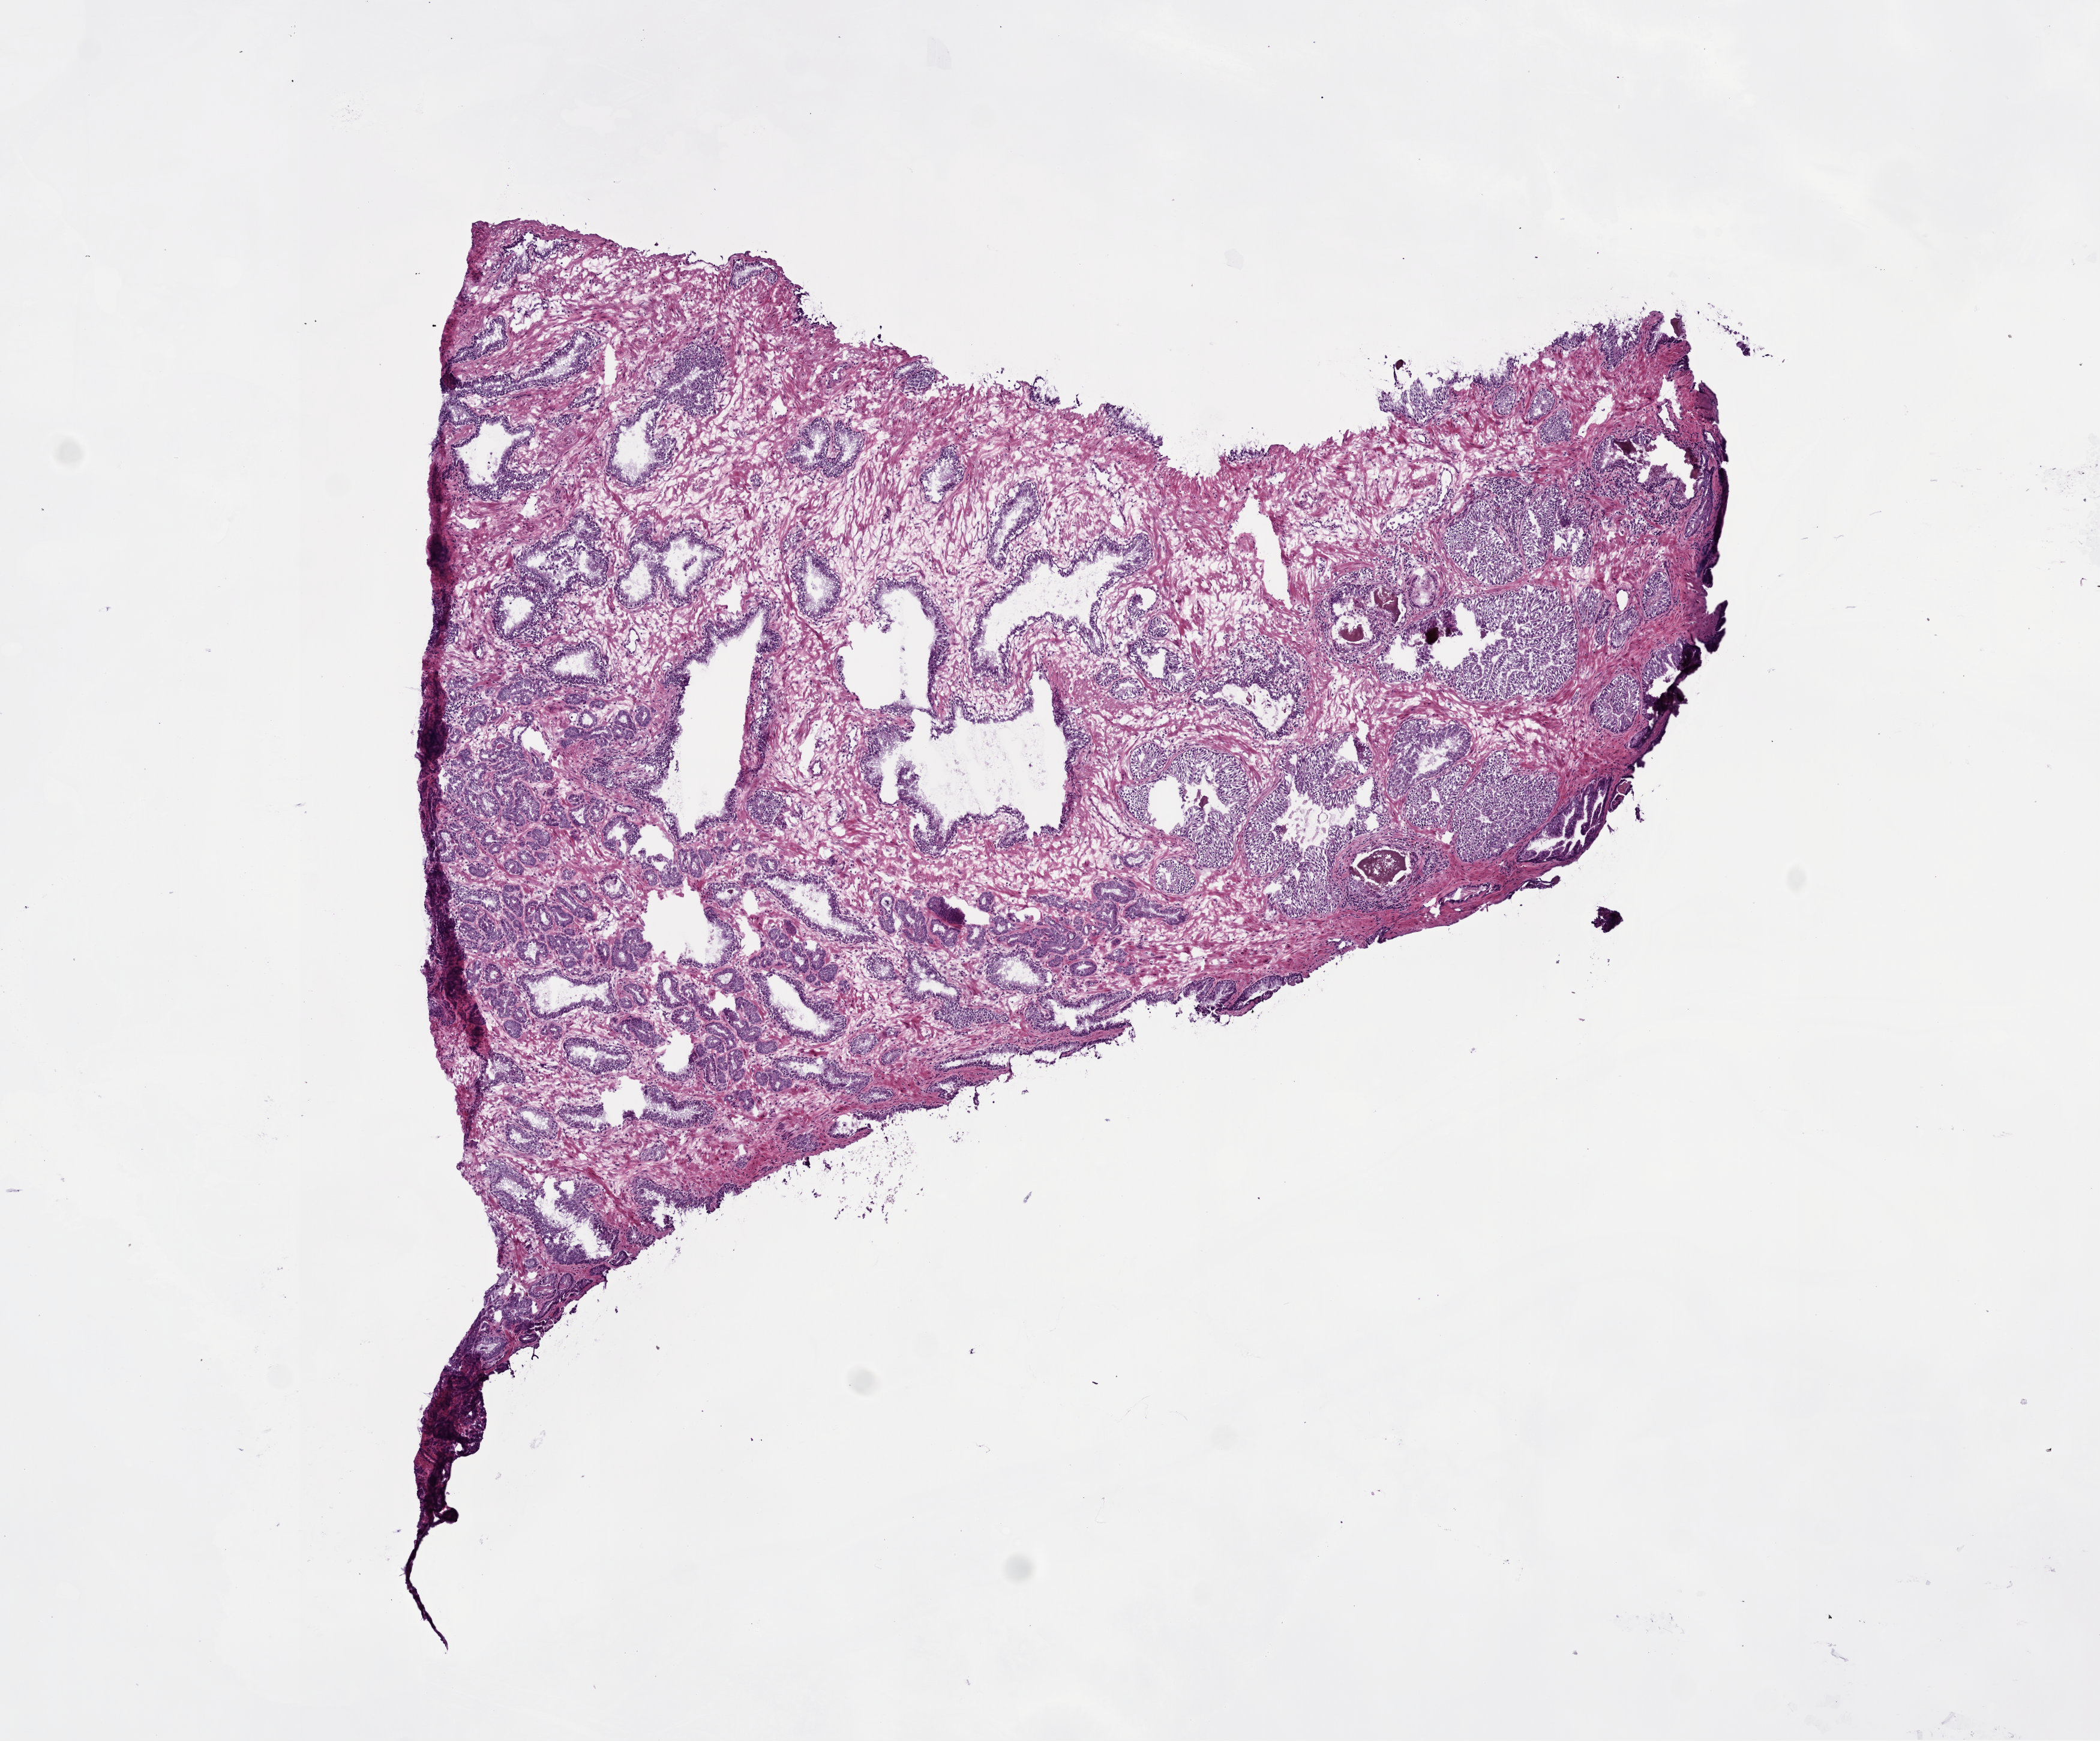
H&E whole-slide image — low-resolution overview of the scanned area, about 7.0 x 5.8 mm (acquisition: 20x scan); frozen section from the bottom of the tissue portion; primary tumour sample from the prostate. Male patient; age at initial diagnosis 59 years. Gleason score: 7 (3+4). Composition of this section per pathologist review: tumour cells 45%, tumour nuclei 45%, normal cells 20%, stromal cells 35%, necrosis 0%. Infiltration values recorded for this section: lymphocyte infiltration 4%, monocyte infiltration 2%, neutrophil infiltration 0%.
• histologic diagnosis: Acinar cell carcinoma (prostate gland)
• lymph nodes positive (case pathology): 0 of 26 examined
• laterality: bilateral